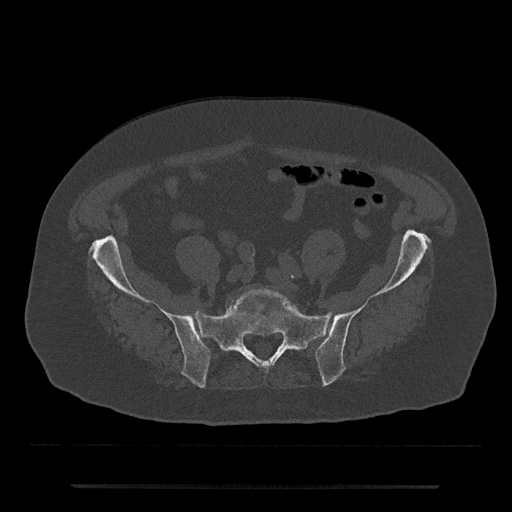
CT including the spine, one axial slice. 120 kVp. Bone window (W 1800 / L 400 HU). 0.5 mm slice thickness. 512 × 512 image matrix, field of view 434 × 434 mm. Male patient, age 80 years. From the clinical record (not read from this slice): primary cancer: prostate; vertebrae with lytic lesions (as recorded): L1, T11.
Outlined on this slice (semi-automatically segmented with operator editing):
- L5 vertebra: bounding box [x1, y1, x2, y2] px = [231, 288, 299, 313]